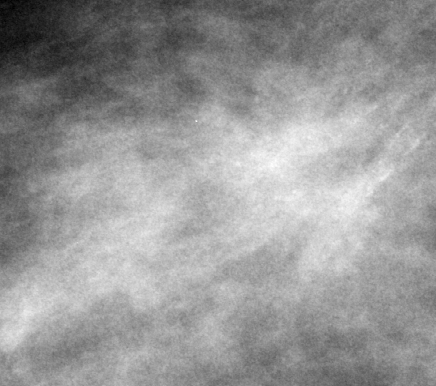
Region of interest cut from a scanned film mammogram (one marked finding), right breast, CC view, BI-RADS breast density category 2 (scale 1–4).
- Mass, shape irregular, margins spiculated; BI-RADS assessment category 5; subtlety rating 5 on a 1 (subtle) to 5 (obvious) scale; pathology result (as recorded, not read from the image): malignant.